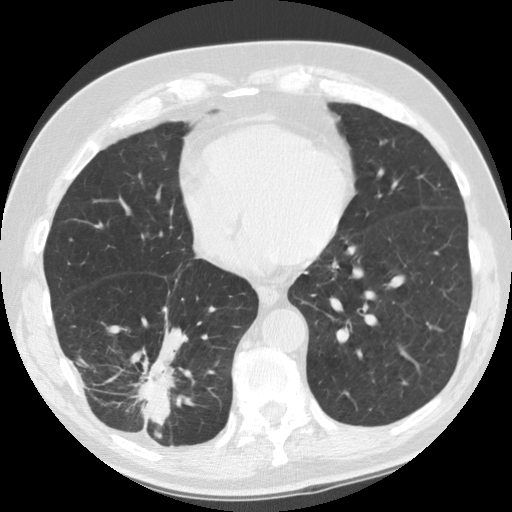
Low-dose screening chest CT, one axial slice; position 42 of 135 along the scan axis; lung window (W 1500 / L -600 HU); 2.5 mm slice thickness; 512 × 512 image matrix, field of view 340 × 340 mm.
Annotated regions visible in this slice (manually delineated by an expert):
- lesion 1 (tumor, lower lobe of right lung): bounding box [x1, y1, x2, y2] px = [134, 358, 174, 426]